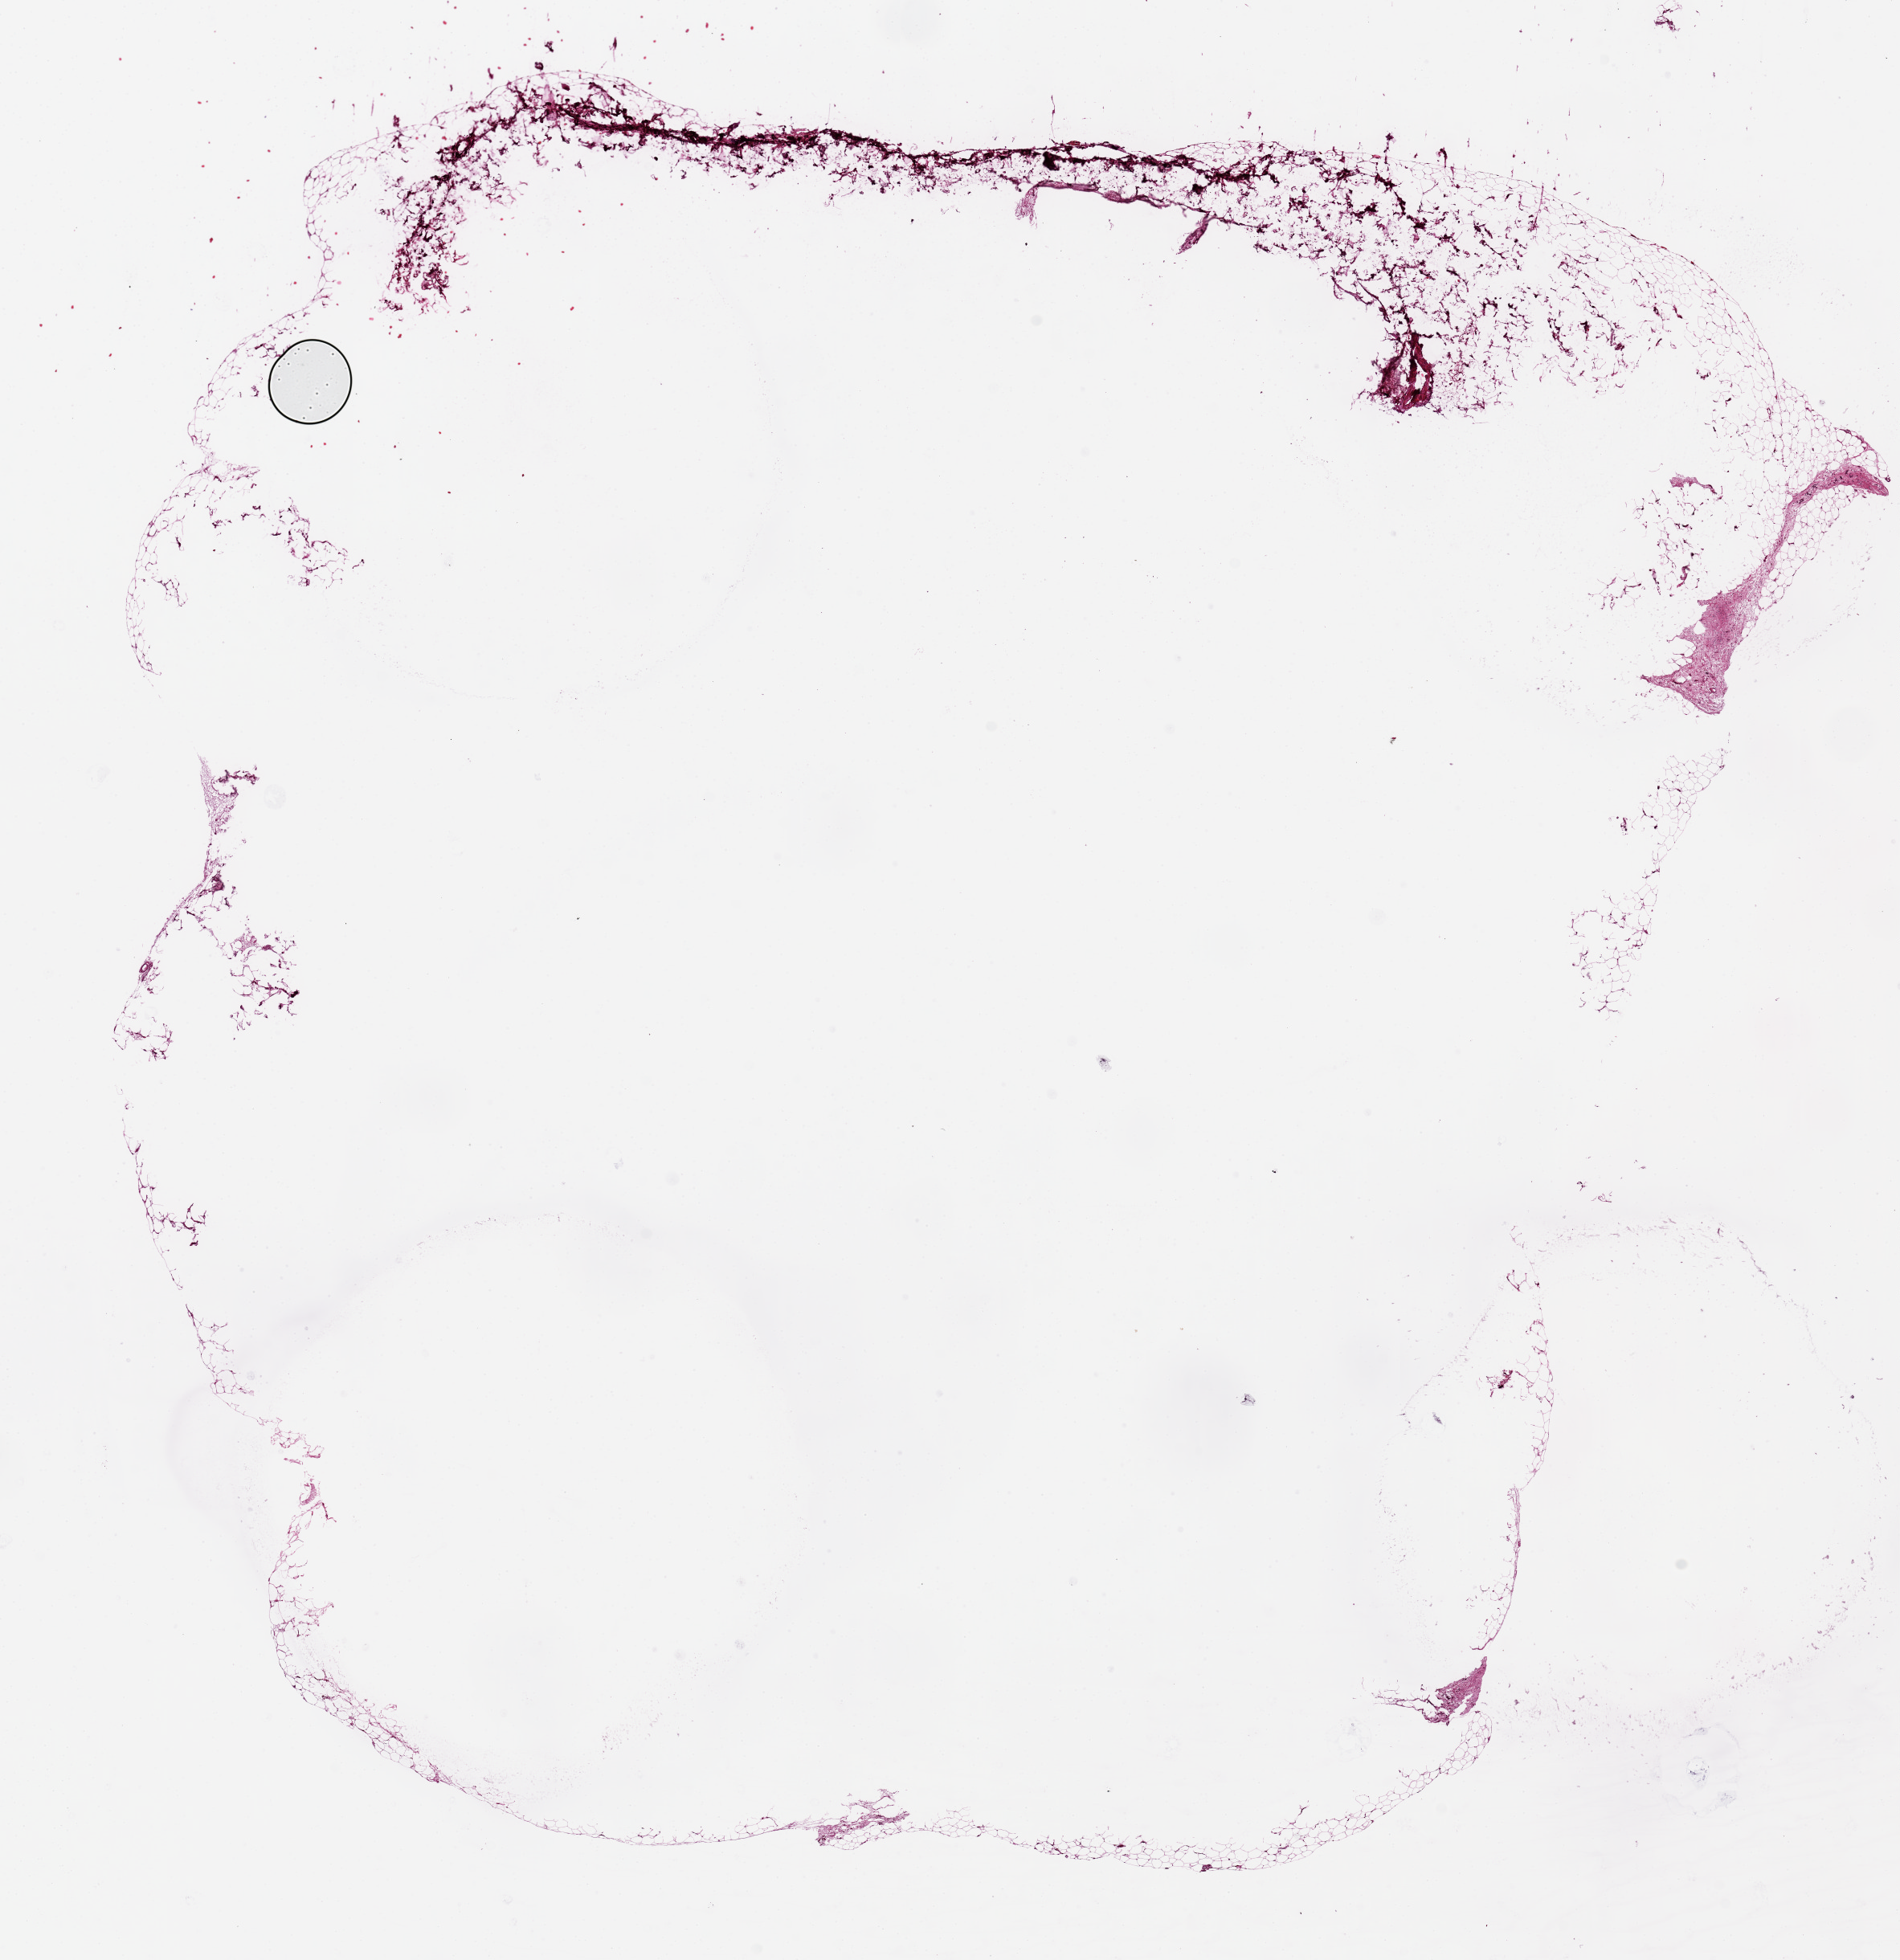
Digitized H&E-stained section, a low-resolution overview of the entire scanned area, about 18.7 x 19.3 mm (acquisition: 20x scan); PAXgene-fixed, paraffin-embedded tissue; section of adipose tissue (target tissue); tissue donor sample.
Reviewer comment on this tissue sample: Central 95% of specimen missing--?poor fixation? (See Request).